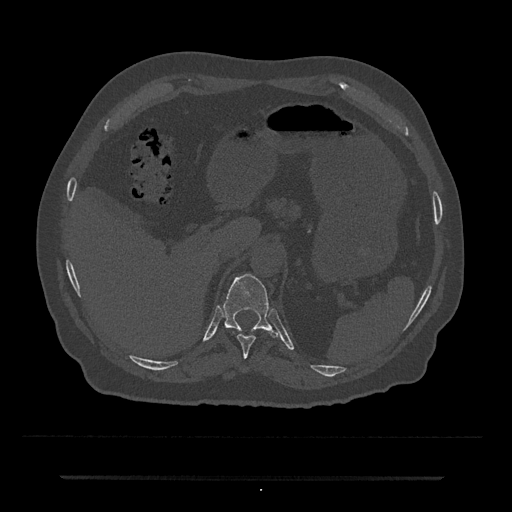
CT including the spine, one axial slice. Slice 199 of 797 in the series (ordered by position). 120 kVp. Bone window (W 1800 / L 400 HU). 0.5 mm slice thickness. 512 × 512 image matrix, field of view 437 × 437 mm. Patient: male, 69 years. Case-level facts recorded for this patient, not image findings: primary cancer: prostate.
Annotated regions visible in this slice (semi-automatically segmented with operator editing):
- T10 vertebra: bounding box (x1, y1, x2, y2) in pixels: (233, 331, 256, 358)
- T11 vertebra: (223, 273, 281, 339)